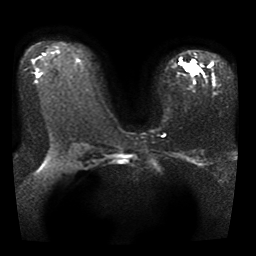
Breast MRI, one axial slice. Position 24 of 41 along the scan axis. Diffusion-weighted series; image 2 of 4 stored at this slice position (different b-values; order by instance number). 1.5 T. 5 mm slice thickness. 256 × 256 image matrix. Female patient.
Annotated regions visible in this slice (manually delineated by an expert):
- tumour on diffusion-weighted imaging: bounding box [x1, y1, x2, y2] px = [178, 61, 198, 74]